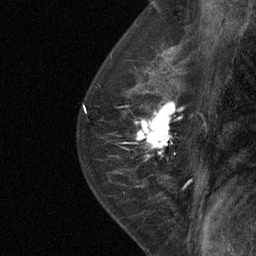
Breast MRI (dynamic contrast-enhanced), one sagittal slice. Slice 44 of 64 in the series (ordered by position). Dynamic contrast-enhanced study with each time point stored as its own series, time point 2 of 4 at this slice position (early post-contrast, ordered by acquisition time). 1.5 T. TE 4.8 ms, TR 27 ms. 256 × 256 image matrix. Patient: female, 50 years. From the clinical record (not read from this slice): setting: breast cancer imaged before/during neoadjuvant chemotherapy; receptor status: HER2-positive.
Structures marked on this image (semi-automatic segmentation, software-assisted and operator-edited):
- analysis volume of interest (the breast-tissue region the enhancement analysis was run in; not a lesion): bounding box <123,91,187,177> (left, top, right, bottom; pixels)
- tumour enhancement mask (voxels above the 90 % enhancement threshold inside the analysis volume of interest): <135,101,182,155>